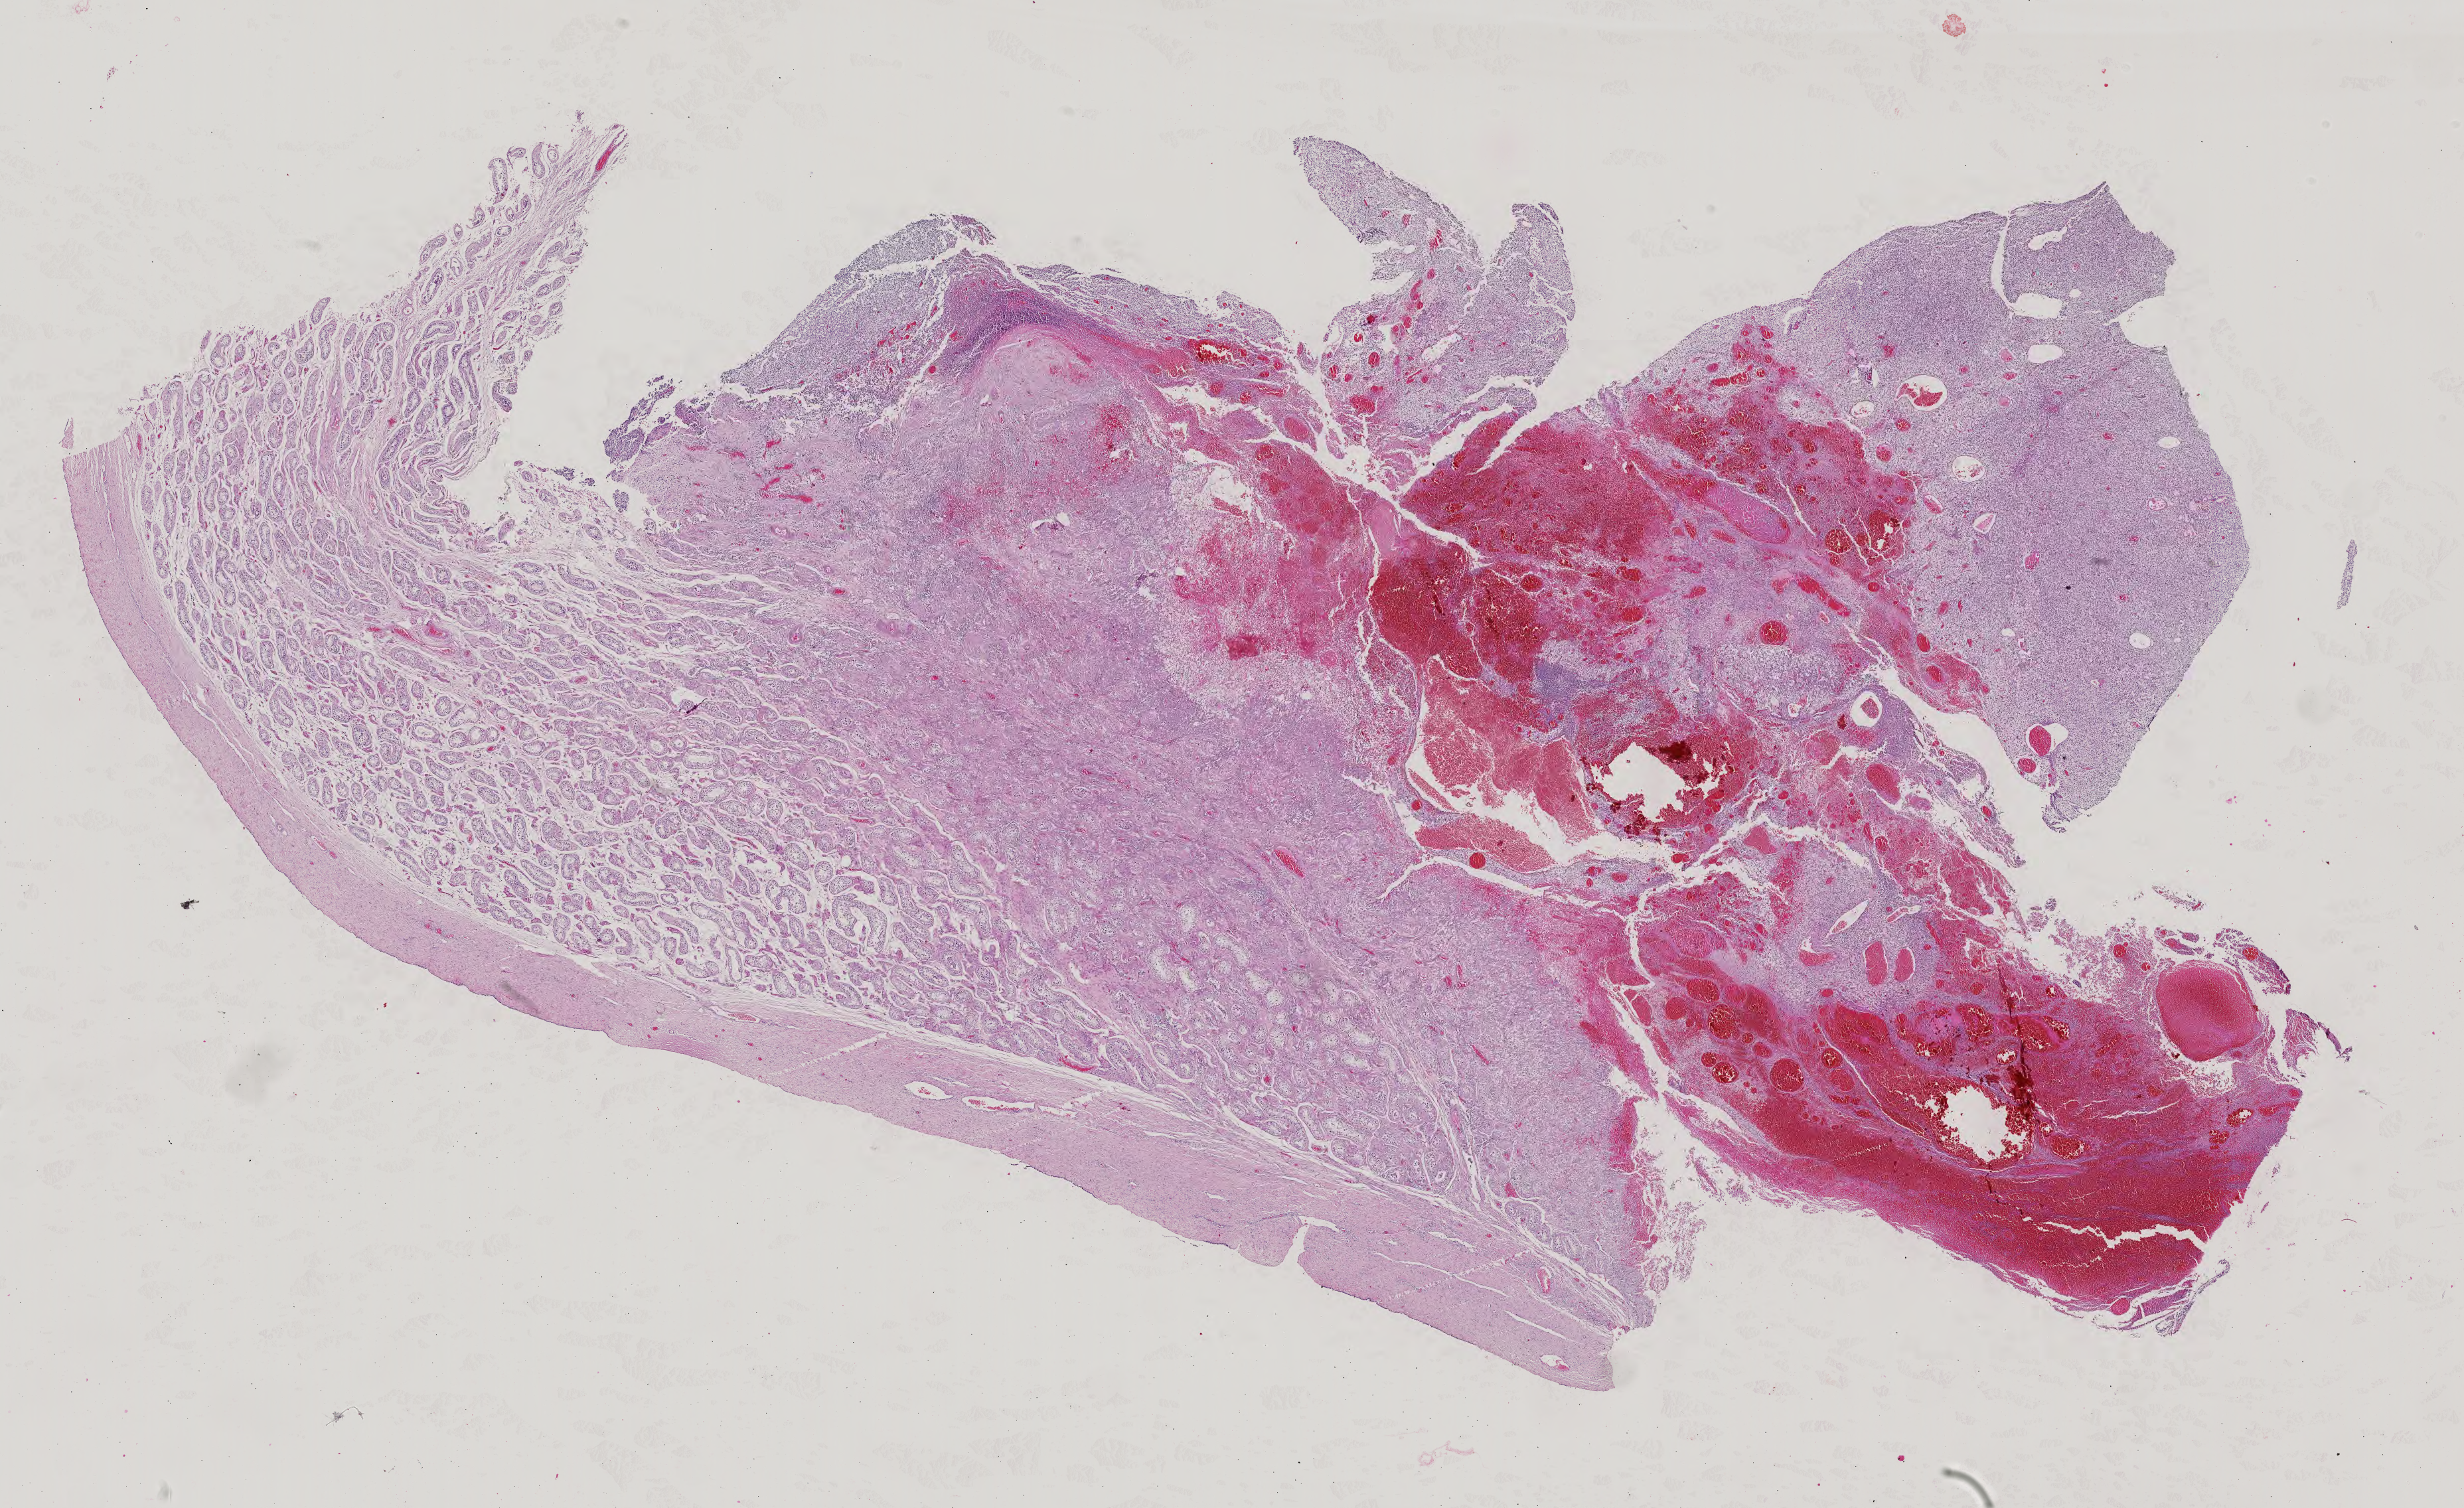
Digitized Hematoxylin and eosin (H&E) stained tissue section (whole slide) — shown as a low-resolution overview of the whole scanned area (about 27.0 x 16.6 mm, acquisition: 40x scan), formalin-fixed paraffin-embedded (FFPE) diagnostic section, primary tumour sample from the testis. Male patient; age at initial diagnosis 34 years.
- laterality: left
- AJCC pathologic stage: II
- pathologic diagnosis: Mixed germ cell tumor